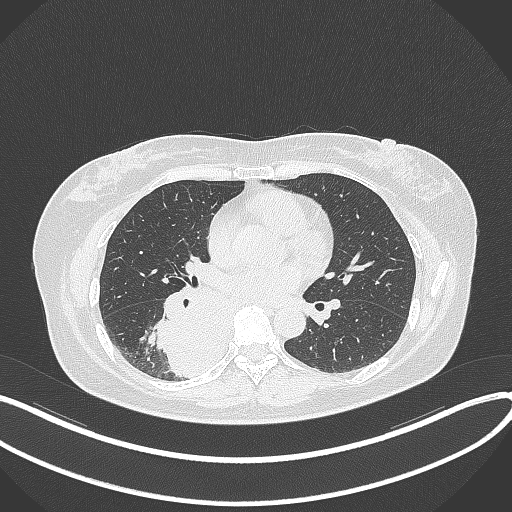
Chest CT, one axial slice; slice 176 of 331 in the series (ordered by position); lung window (W 1500 / L -600 HU); 1 mm slice thickness; 512 × 512 image matrix, field of view 400 × 400 mm. Patient: female, 54 years. From the clinical record (not read from this slice): clinical TNM (as recorded): T4 N0 M0.
Annotated regions visible in this slice (bounding box drawn by a radiologist):
- lung tumour (recorded histology: adenocarcinoma): bounding box <149,284,237,381> (left, top, right, bottom; pixels)